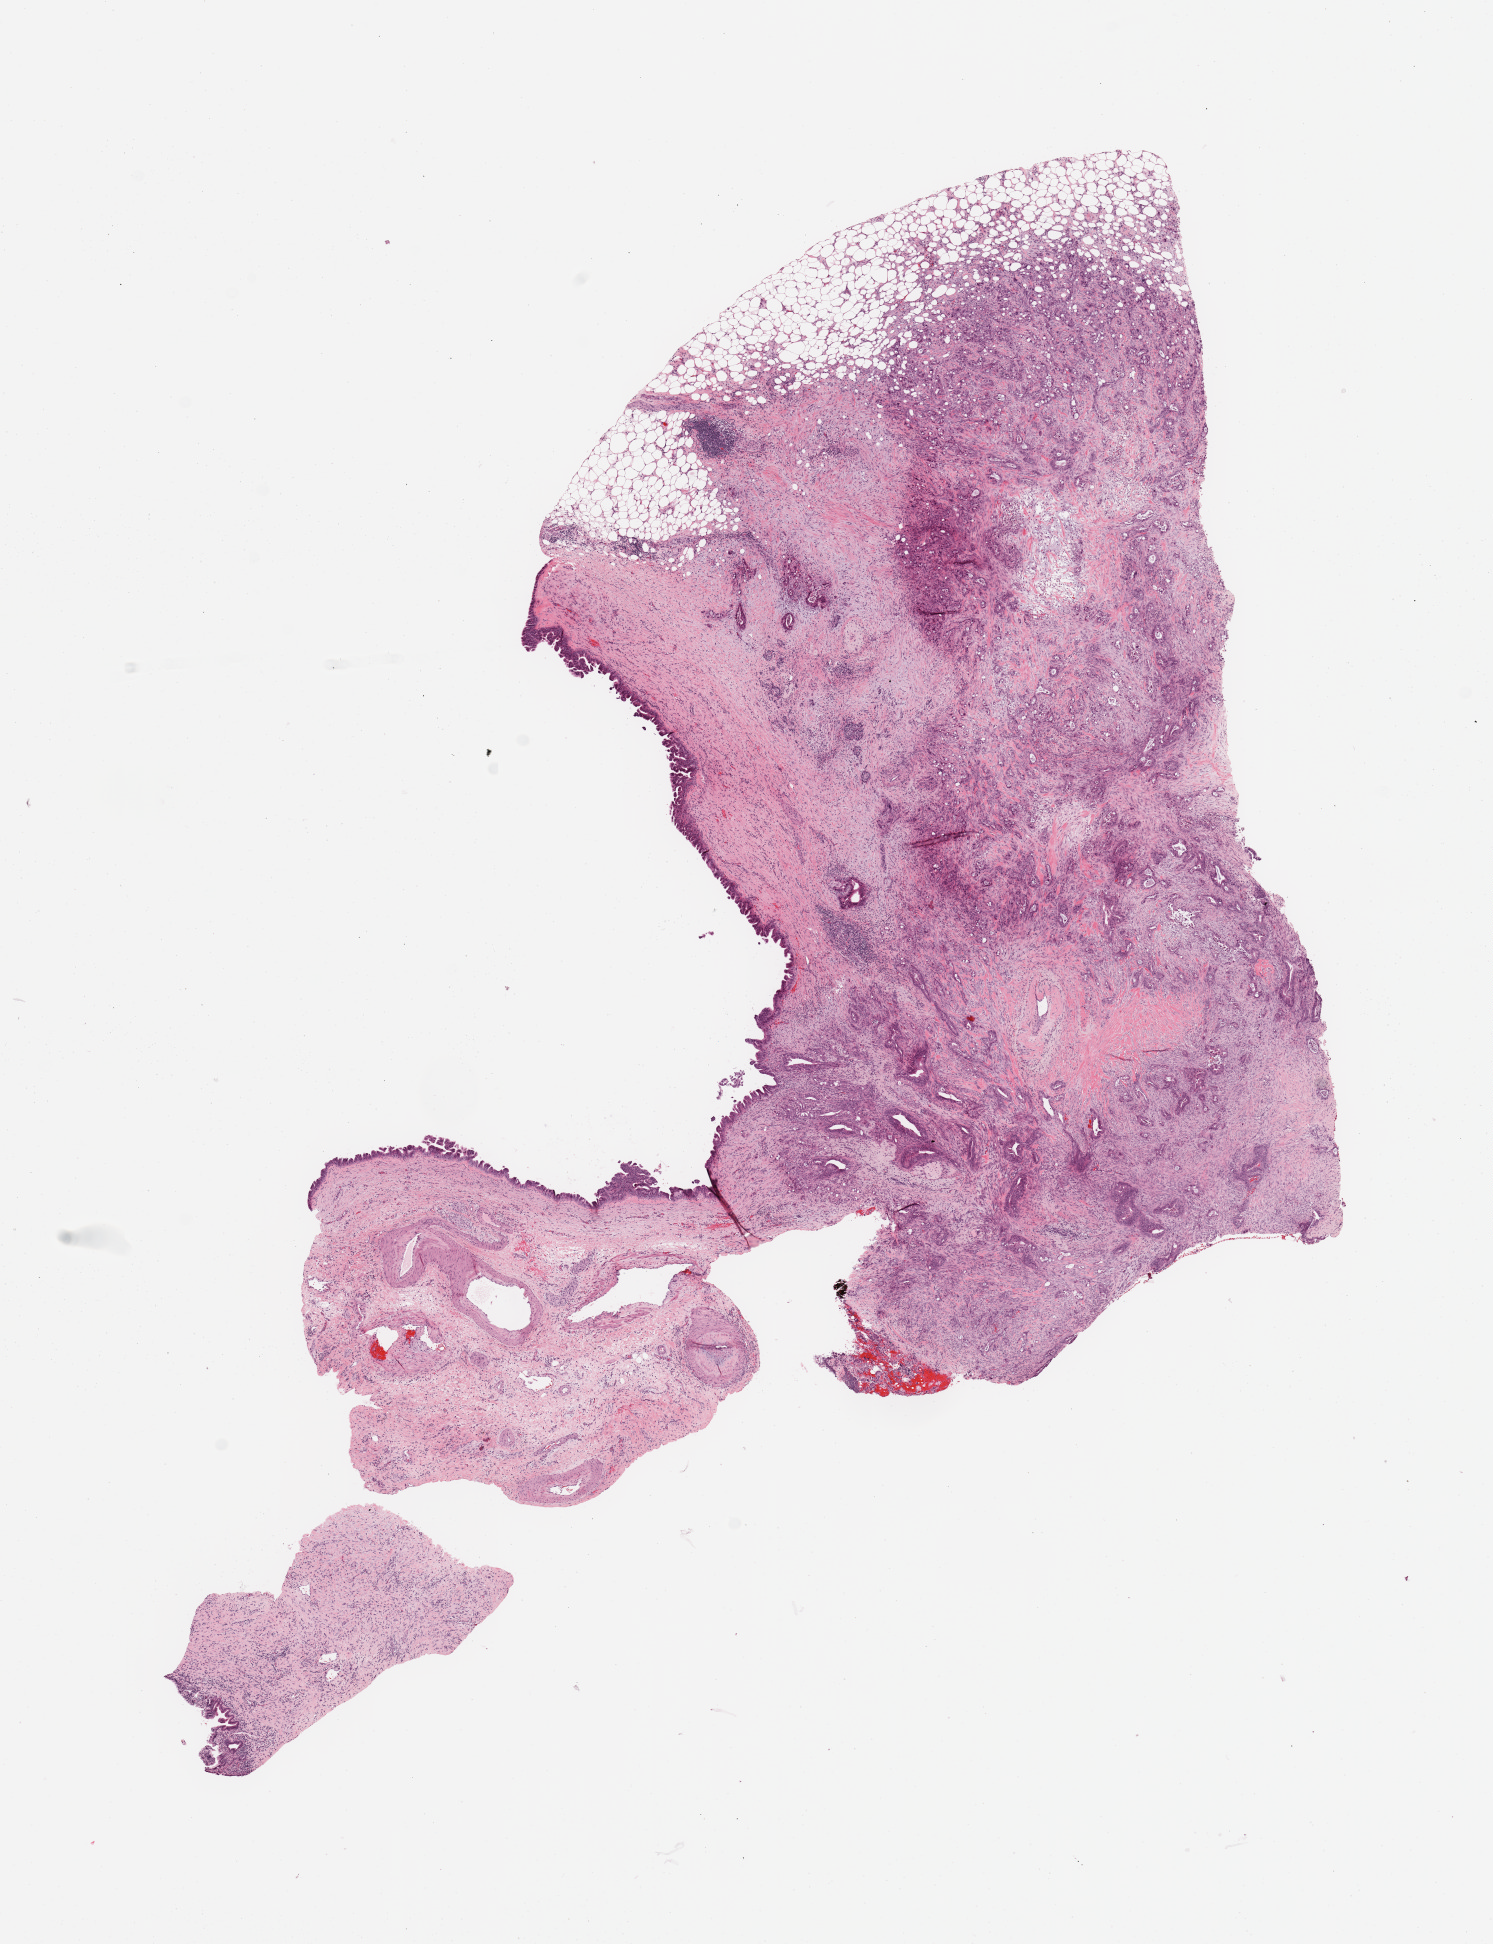
Whole-slide histology image, H&E, shown as a low-resolution overview of the whole scanned area (about 11.8 x 15.4 mm), tumour tissue sample, sampled site: pancreas. Male, 80 y/o. Histologic grade: G2 (moderately differentiated). Composition of this section per pathologist review: tumour nuclei 60%, necrosis 0%.
• AJCC pathologic stage: I
• primary tumour site (as recorded): head
• histologic diagnosis: Infiltrating duct carcinoma, NOS